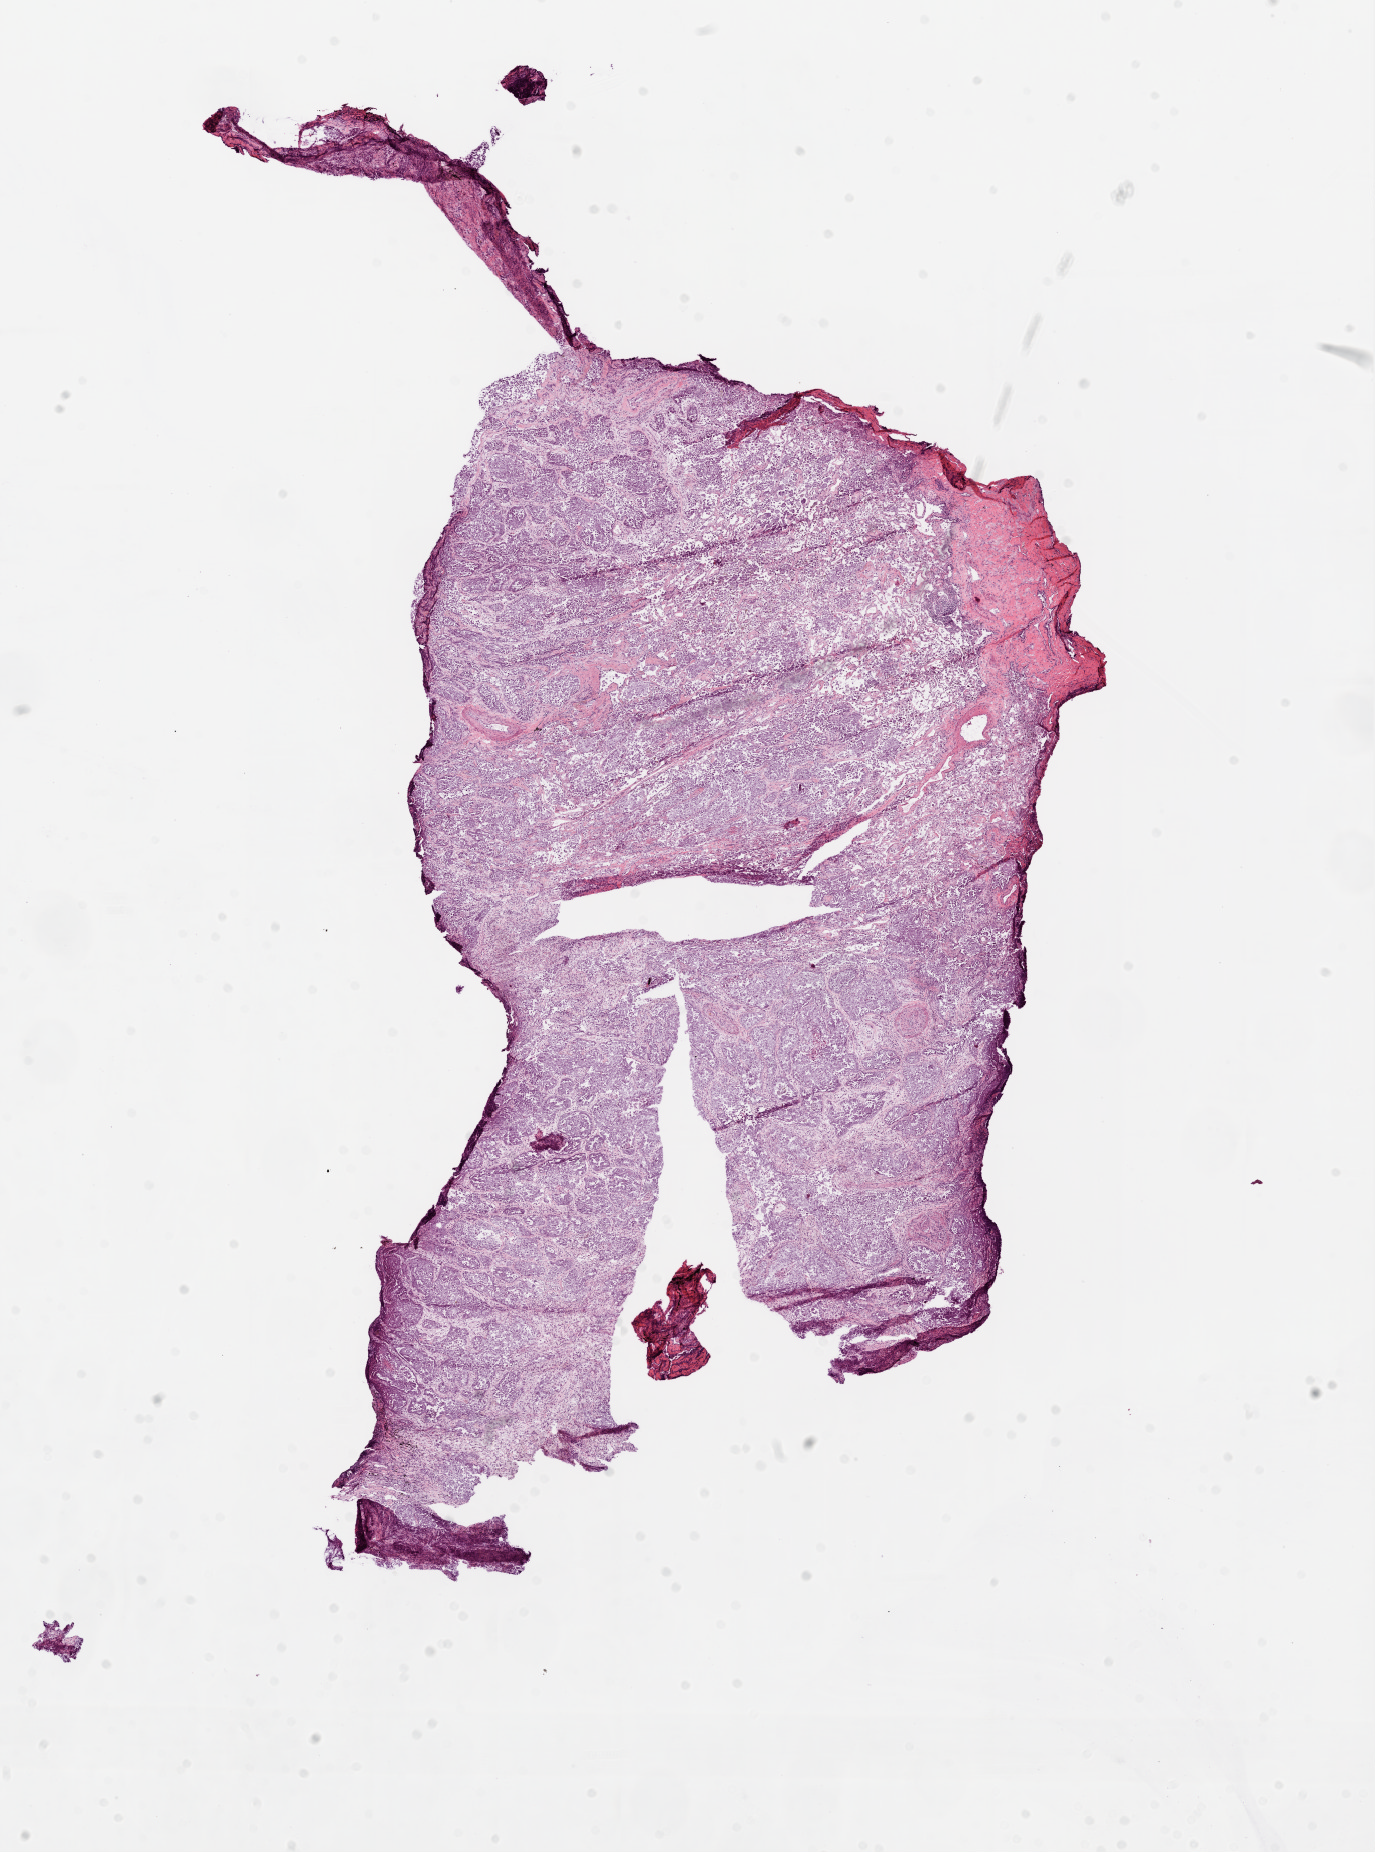
Hematoxylin and eosin (H&E) stained whole-slide image, a low-resolution overview of the entire scanned area, about 11.0 x 14.9 mm; frozen section; lung, primary tumour sample. Male, age 45 years at initial diagnosis.
Pathologic diagnosis: Adenocarcinoma, NOS (upper lobe, lung).